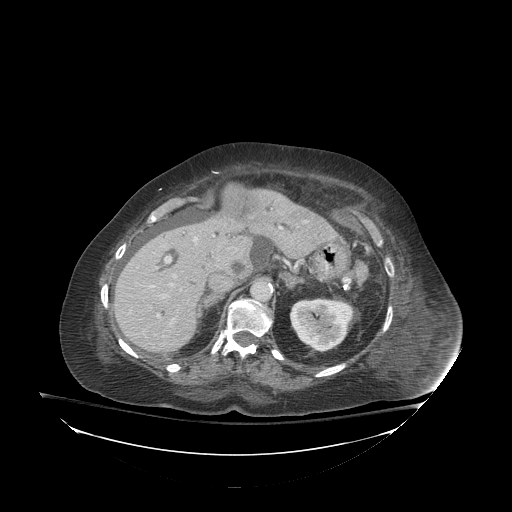
Contrast-enhanced abdominal CT (liver protocol), one axial slice; slice 55 of 81 in the series (ordered by position); reconstruction kernel STANDARD; soft-tissue window (W 400 / L 40 HU); 2.5 mm slice thickness; 512 × 512 image matrix, field of view 500 × 500 mm. From the clinical record (not read from this slice): diagnosis: hepatocellular carcinoma (patient treated with transarterial chemoembolisation; whether this scan precedes or follows treatment is not stated here); TNM stage (as recorded): Stage-I; Child-Pugh class: B; tumour differentiation: well-moderately differentiated; tumour nodularity: uninodular.
Structures marked on this image (semi-automatically segmented with operator editing):
- liver parenchyma outside the tumour (the mass and vessels are separate outlines, so this box may not span the whole liver): box from (x=114, y=190) to (x=334, y=352) px
- mass: (x=222, y=185)–(x=263, y=220)
- liver vessels: (x=149, y=237)–(x=198, y=321)